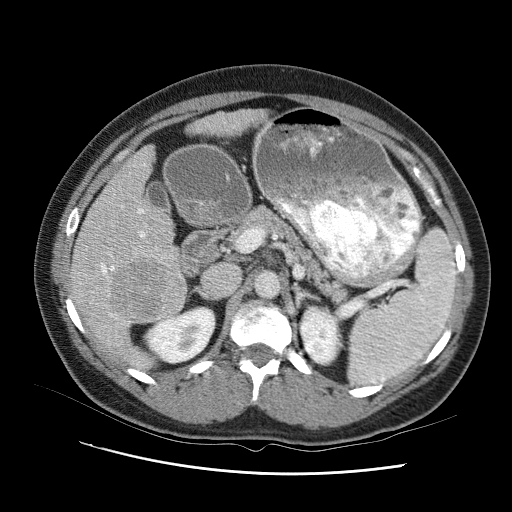
Contrast-enhanced abdominal CT (liver protocol), one axial slice; slice 49 of 95 in the series (ordered by position); reconstruction kernel STANDARD; one of 2 acquisitions stored at this slice position; soft-tissue window (W 400 / L 40 HU); 512 × 512 image matrix, field of view 360 × 360 mm. From the clinical record (not read from this slice): diagnosis: hepatocellular carcinoma (patient treated with transarterial chemoembolisation; whether this scan precedes or follows treatment is not stated here); TNM stage (as recorded): Stage-I; Child-Pugh class: B; tumour differentiation: moderately differentiated; tumour nodularity: uninodular.
Outlined on this slice (semi-automatic segmentation, software-assisted and operator-edited):
- liver parenchyma outside the tumour (the mass and vessels are separate outlines, so this box may not span the whole liver): bounding box <66,102,274,371> (left, top, right, bottom; pixels)
- mass: <118,252,190,317>
- liver vessels: <103,173,188,338>